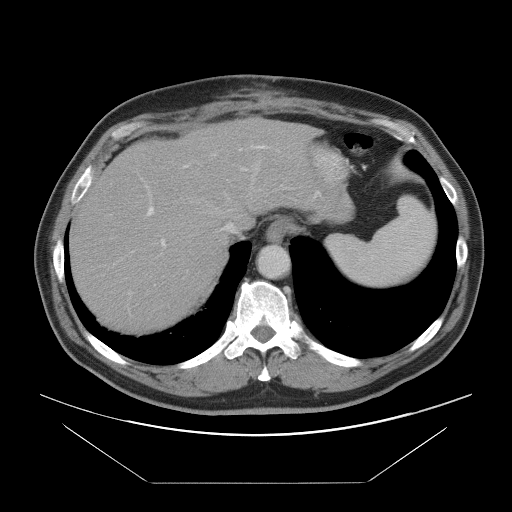
Contrast-enhanced abdominal CT, one axial slice; 120 kVp; intravenous contrast given; soft-tissue window (W 400 / L 40 HU); 5 mm slice thickness; 512 × 512 image matrix. Male patient, age 62 years. Case-level facts recorded for this patient, not image findings: diagnosis: colorectal cancer liver metastases, imaged before liver resection; multiple liver metastases: no; largest metastasis: 7 cm; chemotherapy before resection: yes.
Annotated regions visible in this slice (outlined manually by an expert reader):
- hepatic veins: box from (x=190, y=146) to (x=291, y=233) px
- liver: (x=72, y=121)–(x=315, y=331)
- planned liver remnant (the part of the liver to remain after resection): (x=72, y=170)–(x=227, y=331)
- portal vein (with intrahepatic branches): (x=129, y=146)–(x=265, y=294)